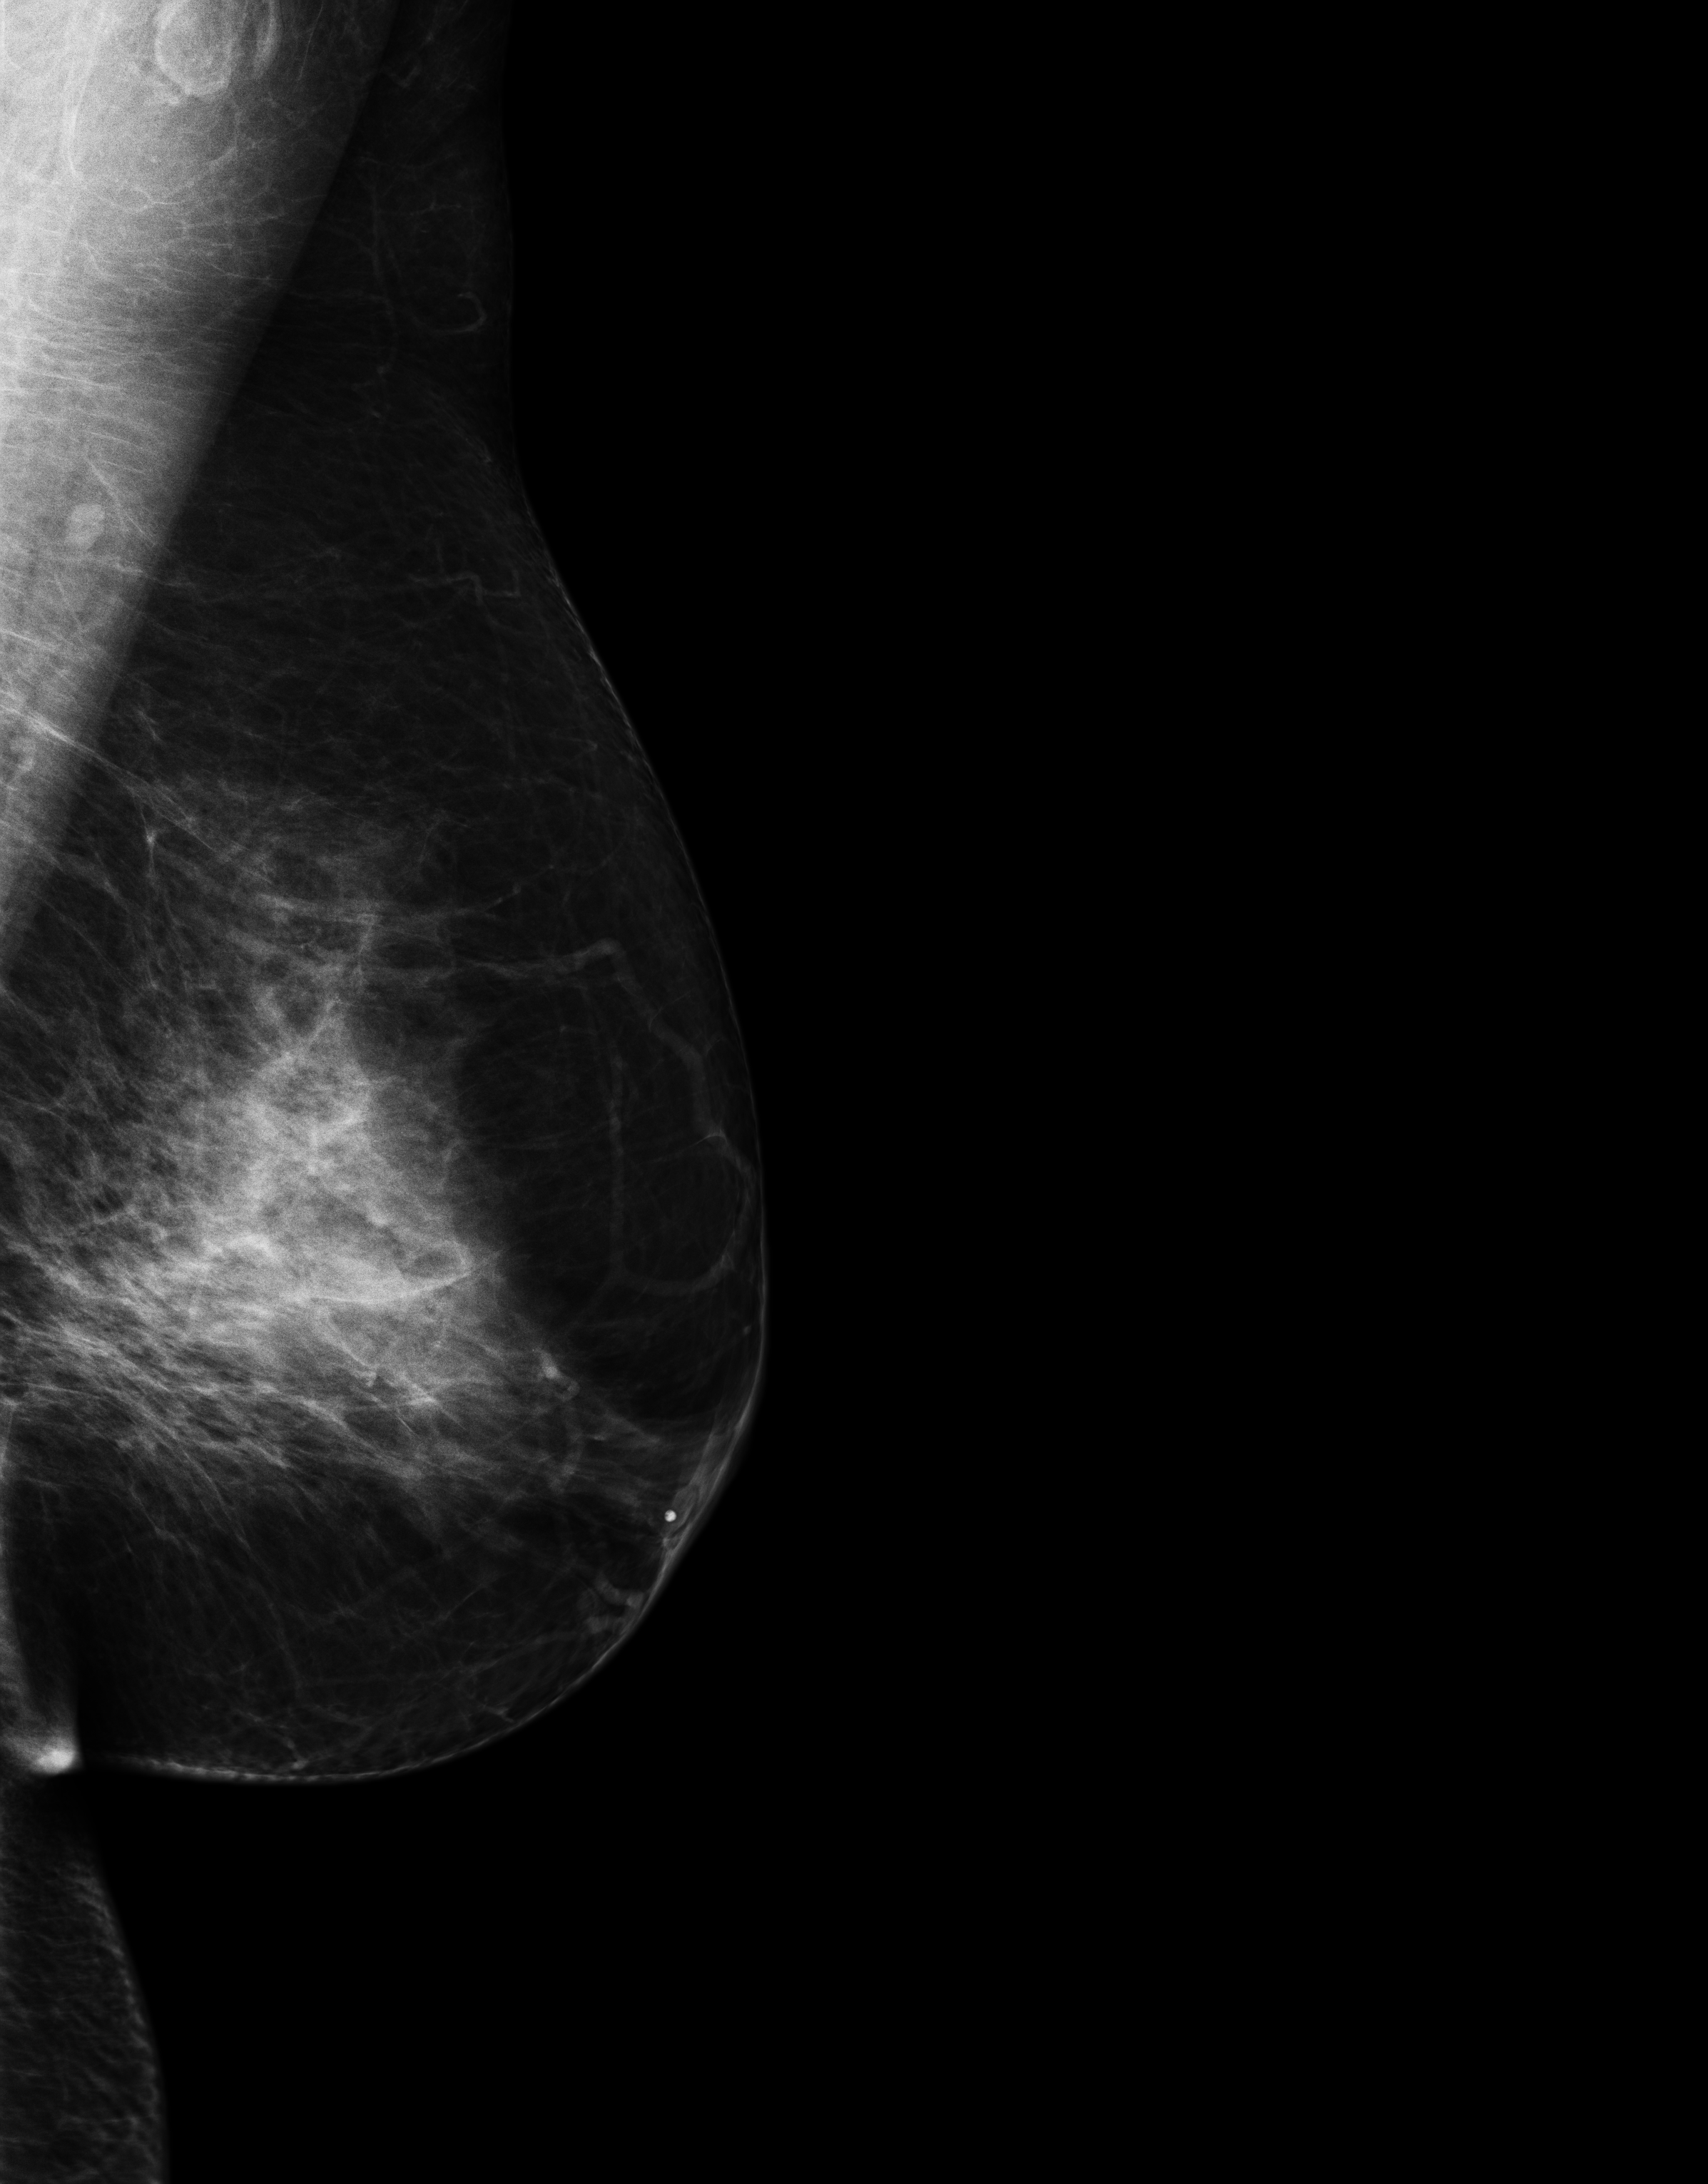
Full-field digital mammogram (FFDM); left breast; medio-lateral oblique projection; annual screening mammography examination; system: Senographe Essential ADS_56.21.3. Patient aged 47 years (female).
BI-RADS breast density category at the screening exam (both breasts, scale 1–4): 3. Final BI-RADS assessment for this screening round (tomosynthesis exam, both breasts): category 1. Recall: no recall after this screen.